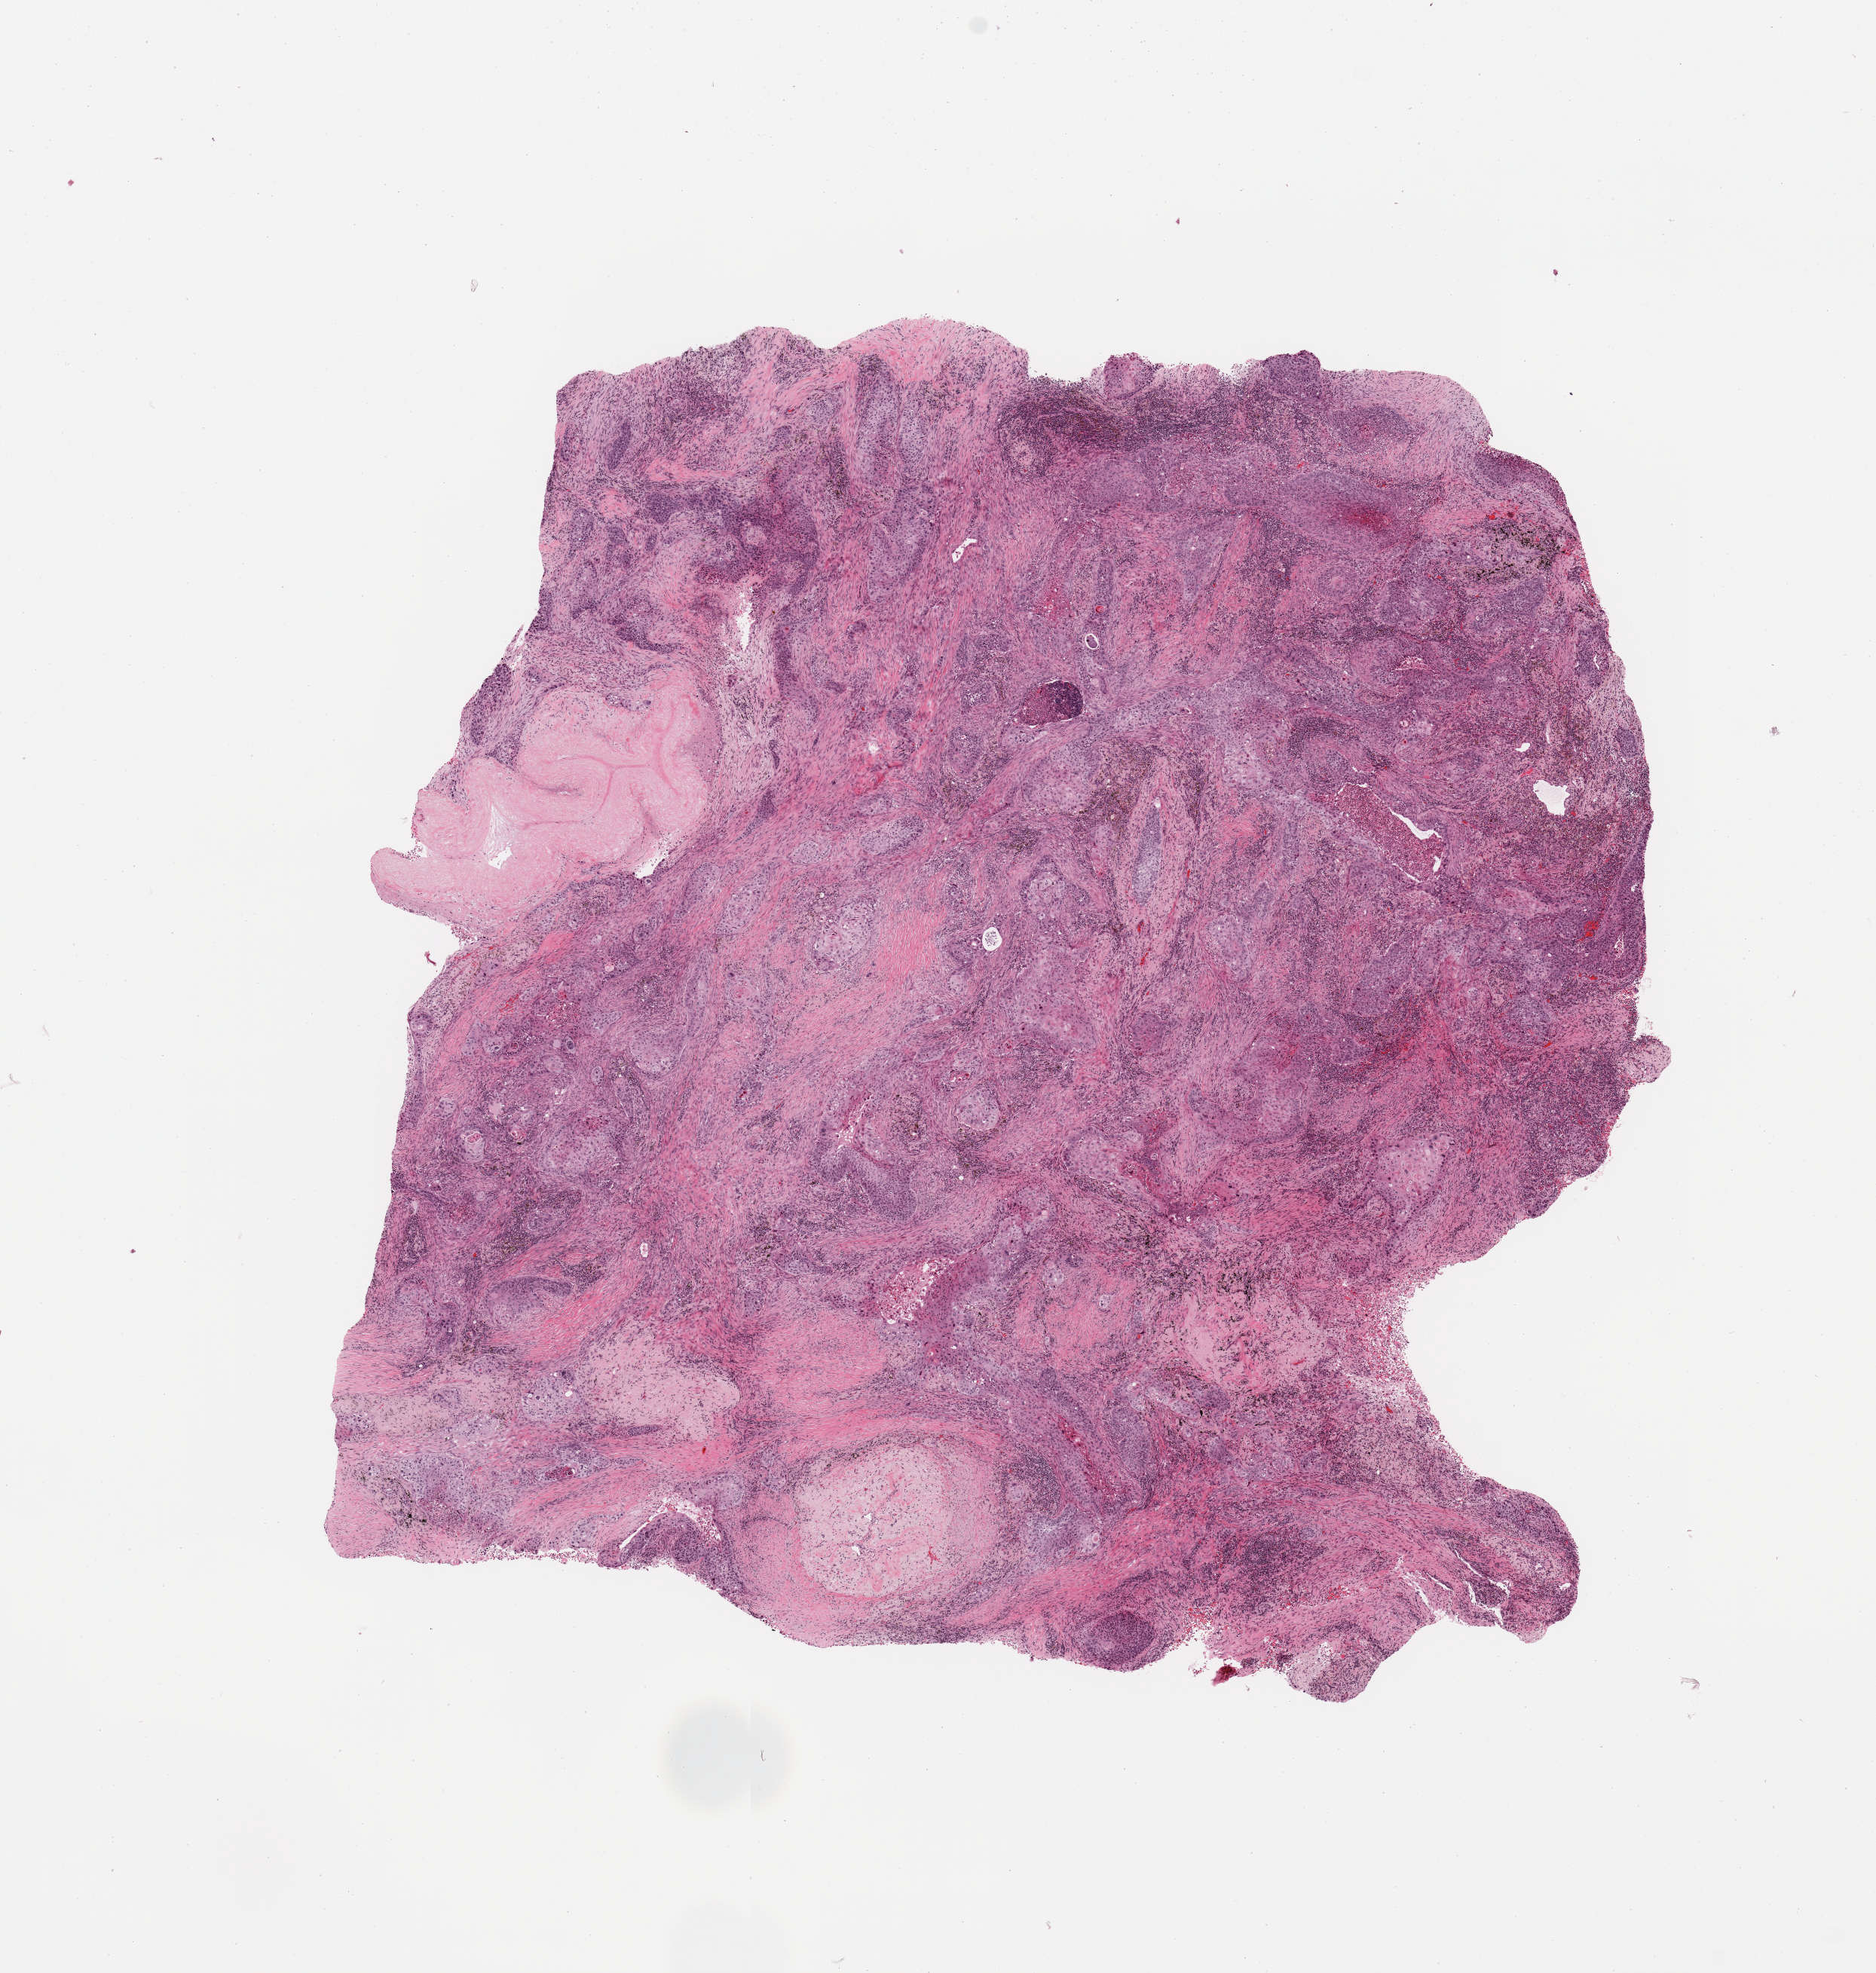
H&E whole-slide image, shown as a low-resolution overview of the whole scanned area (about 9.8 x 10.4 mm), lung, tumour tissue. 61-year-old male patient. Histologic grade: G2 (moderately differentiated).
* histologic diagnosis: Squamous cell carcinoma, NOS
* AJCC pathologic stage: IIA
* primary tumour site (as recorded): left lower lobe